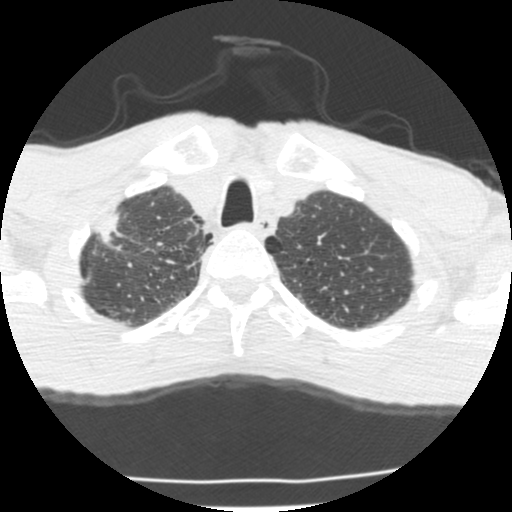
Chest CT (low-dose screening protocol), one axial image. Second screening round (one year after baseline). Lung window (W 1500 / L -600 HU). Standard (soft-tissue) reconstruction kernel (STANDARD). 120 kVp. Male participant, aged 62 years at enrolment.
- Expert-annotated lung lesion, bounding box (x1, y1, x2, y2) in pixels: (71, 213, 140, 273).
- The exam's reader record, not a measurement of the box and not confirmed to be the same lesion: non-calcified nodule or mass ≥4 mm, right upper lobe, 23 × 11 mm, spiculated (stellate) margins, soft tissue attenuation, pre-existing on the prior screen: yes.
- Official screen result: positive, change unspecified: nodule(s) >= 4 mm or enlarging nodule(s), mass(es), or other non-specific abnormalities suspicious for lung cancer.